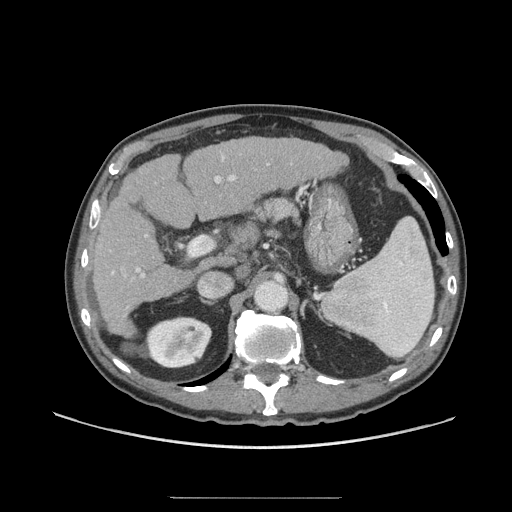
Contrast-enhanced abdominal CT (liver protocol), one axial slice; slice 39 of 71 in the series (ordered by position); soft-tissue window (W 400 / L 40 HU); 2.5 mm slice thickness; 512 × 512 image matrix, field of view 400 × 400 mm. Case-level facts recorded for this patient, not image findings: diagnosis: hepatocellular carcinoma (patient treated with transarterial chemoembolisation; whether this scan precedes or follows treatment is not stated here); TNM stage (as recorded): Stage-I; Child-Pugh class: A; tumour nodularity: uninodular.
Annotated regions visible in this slice (semi-automatic segmentation, software-assisted and operator-edited):
- liver parenchyma outside the tumour (the mass and vessels are separate outlines, so this box may not span the whole liver): box from (x=91, y=136) to (x=347, y=336) px
- liver vessels: (x=111, y=156)–(x=269, y=278)